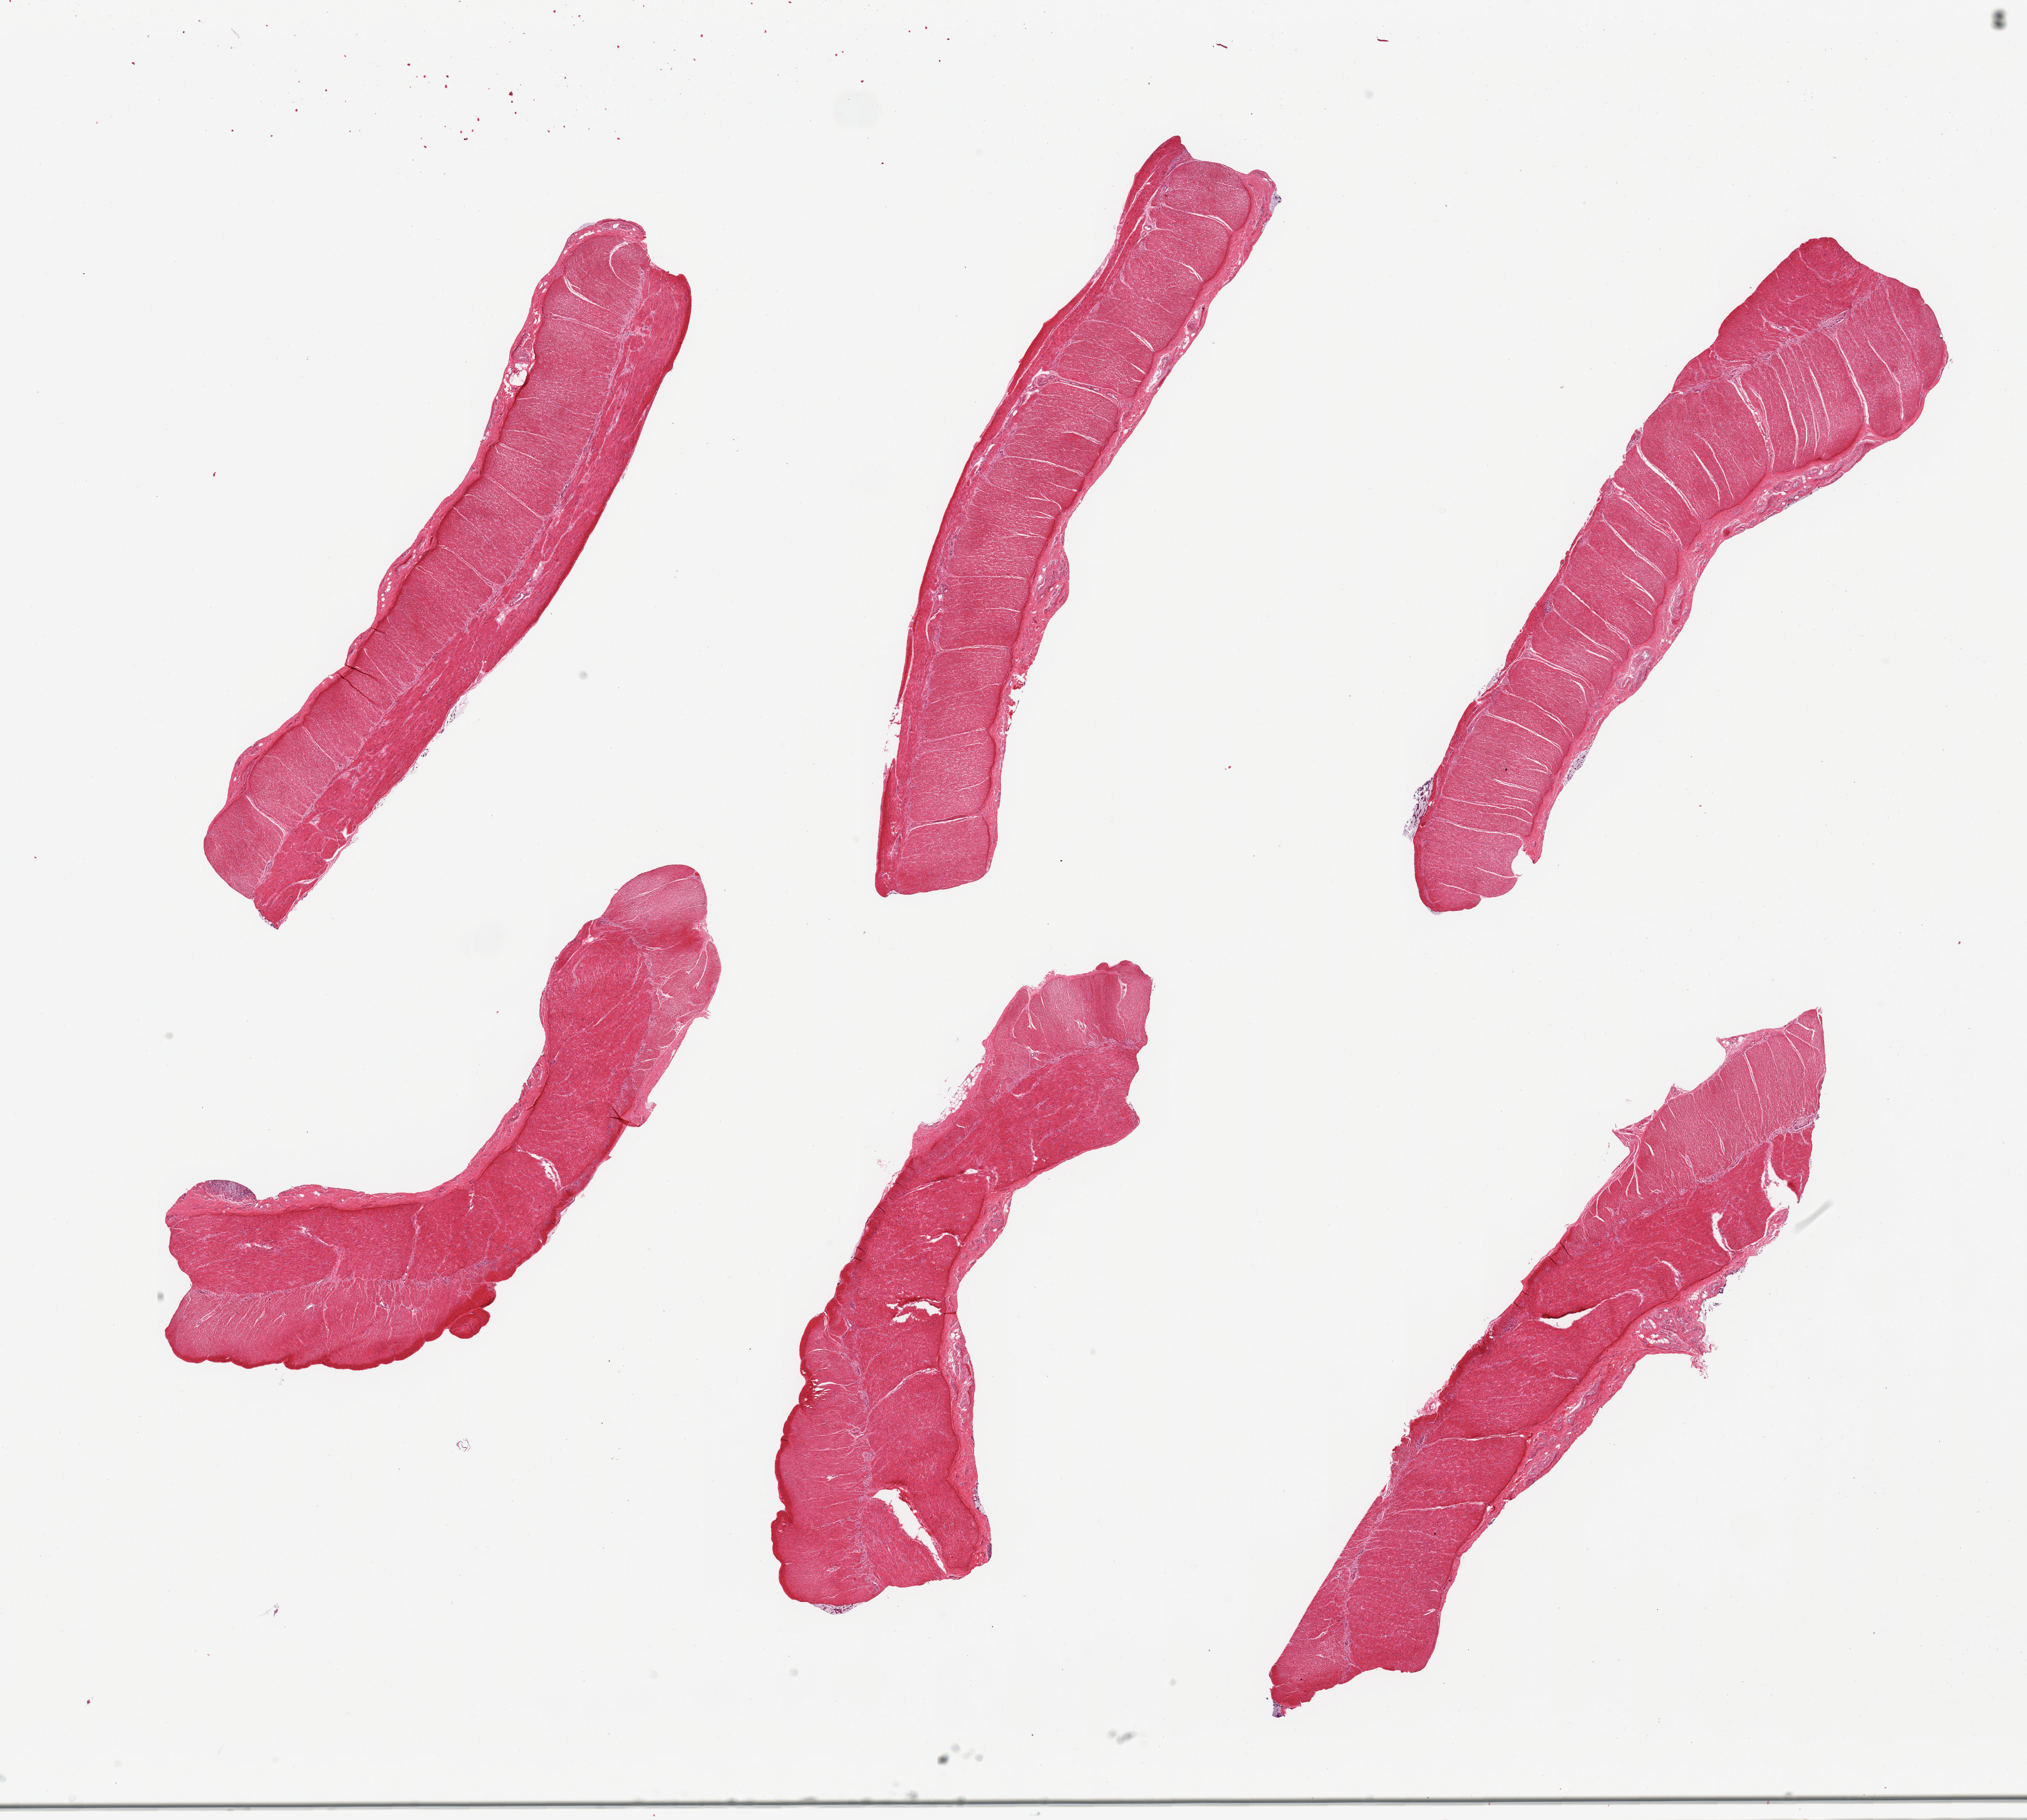
Haematoxylin and eosin whole-slide image, brightfield, a low-resolution overview of the entire scanned area, about 25.6 x 23.0 mm. PAXgene-fixed paraffin-embedded (PFPE) section. Section of sigmoid colon (target tissue). Tissue donor sample. Donor: male.
Review note (as recorded): 6 pieces; well dissected muscularis.